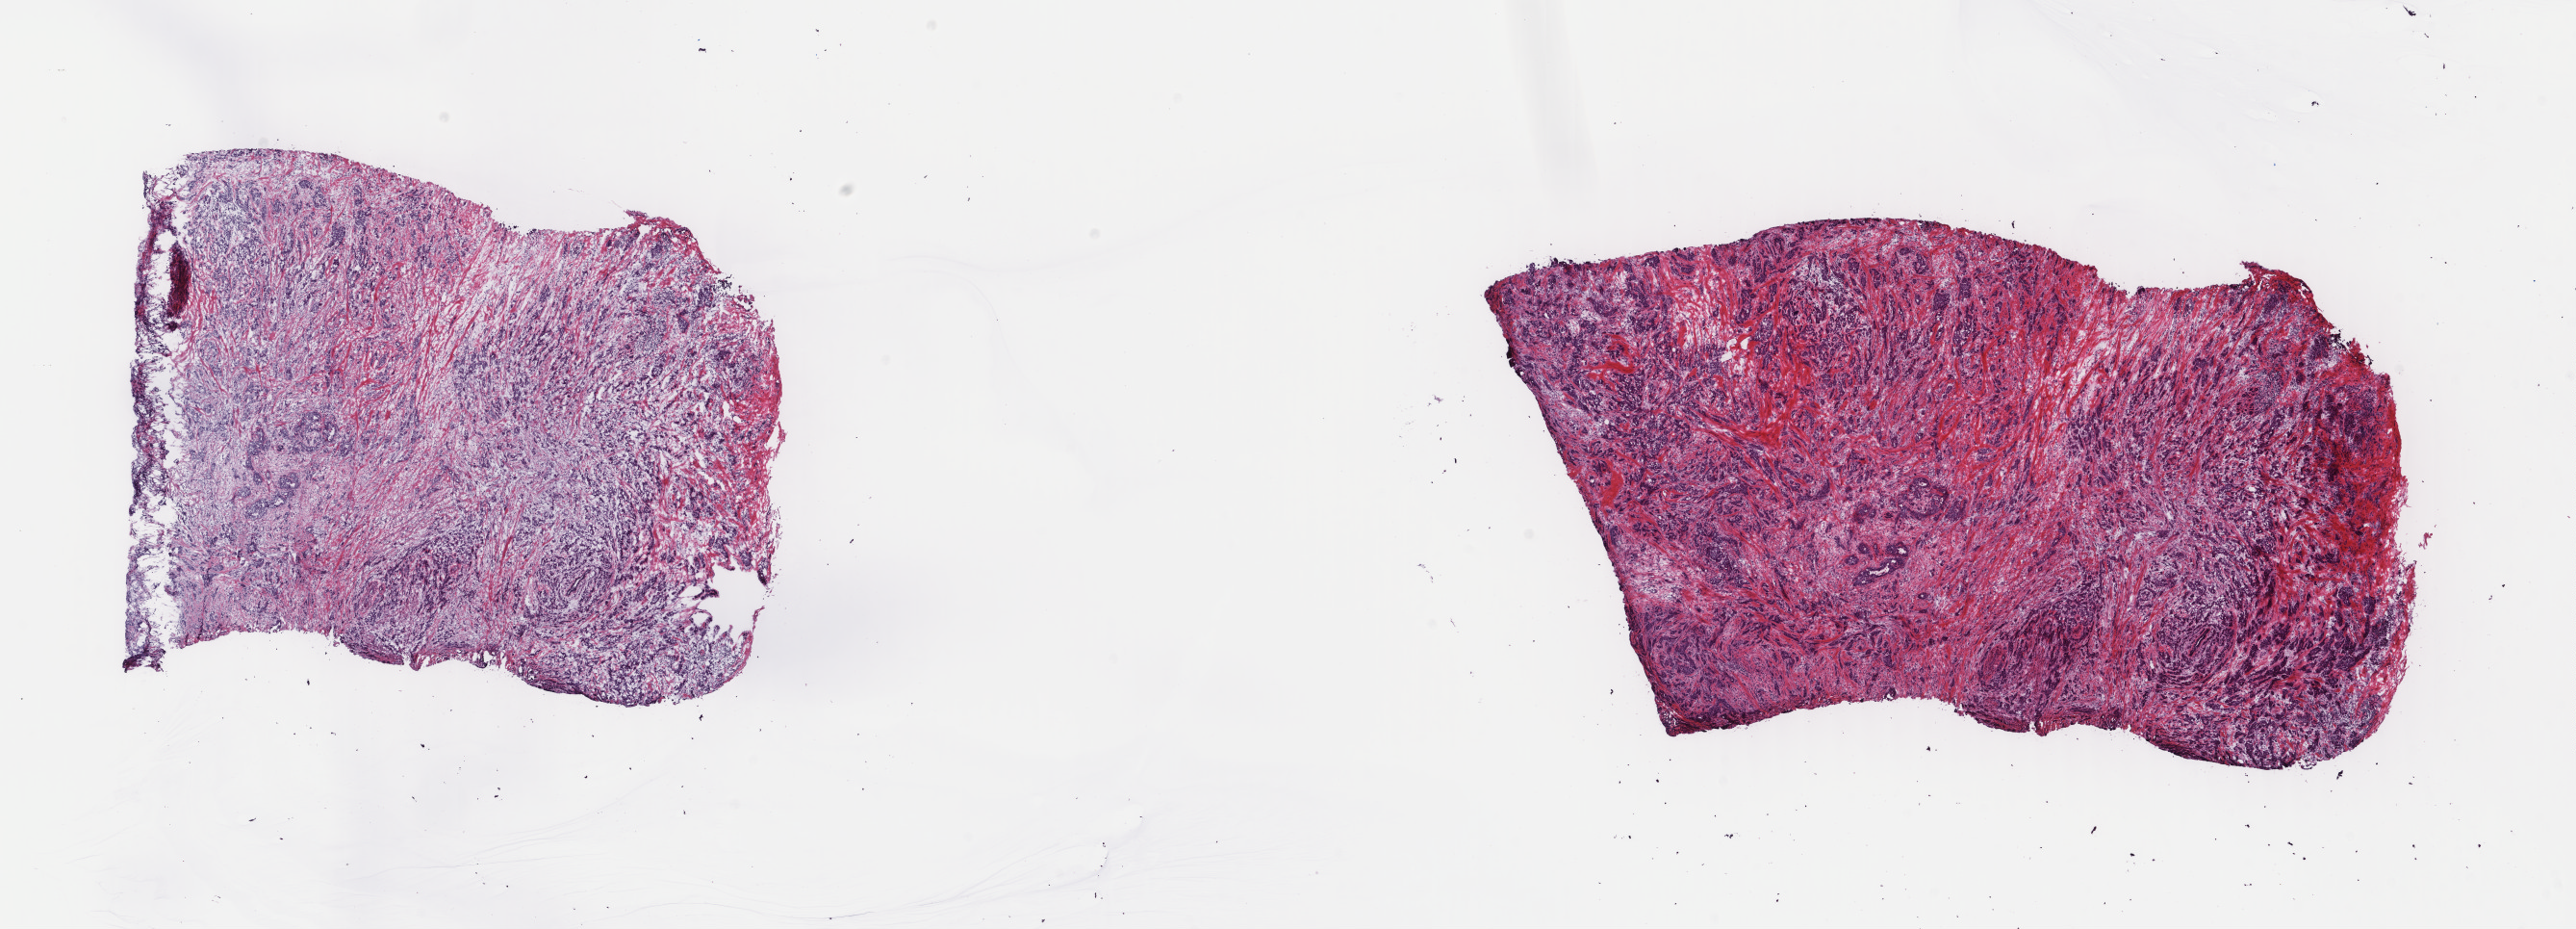
Whole-slide histology image, H&E — shown as a low-resolution overview of the whole scanned area (about 21.2 x 7.7 mm, acquisition: 40x scan). Frozen section from the top of the tissue portion. Breast, primary tumour sample. Female, age 59 years at initial diagnosis. Pathologist review of this section (percent, as recorded): tumour cells 100%, tumour nuclei 75%, normal cells 0%, stromal cells 0%, necrosis 0%. Inflammatory infiltration, as recorded: lymphocyte infiltration 0%, monocyte infiltration 0%, neutrophil infiltration 0%.
- lymph nodes positive (case pathology): 4 of 11 examined
- pathologic diagnosis: Infiltrating duct carcinoma, NOS
- AJCC pathologic stage: IIIA (7th edition)
- TNM: T2 N2a M0